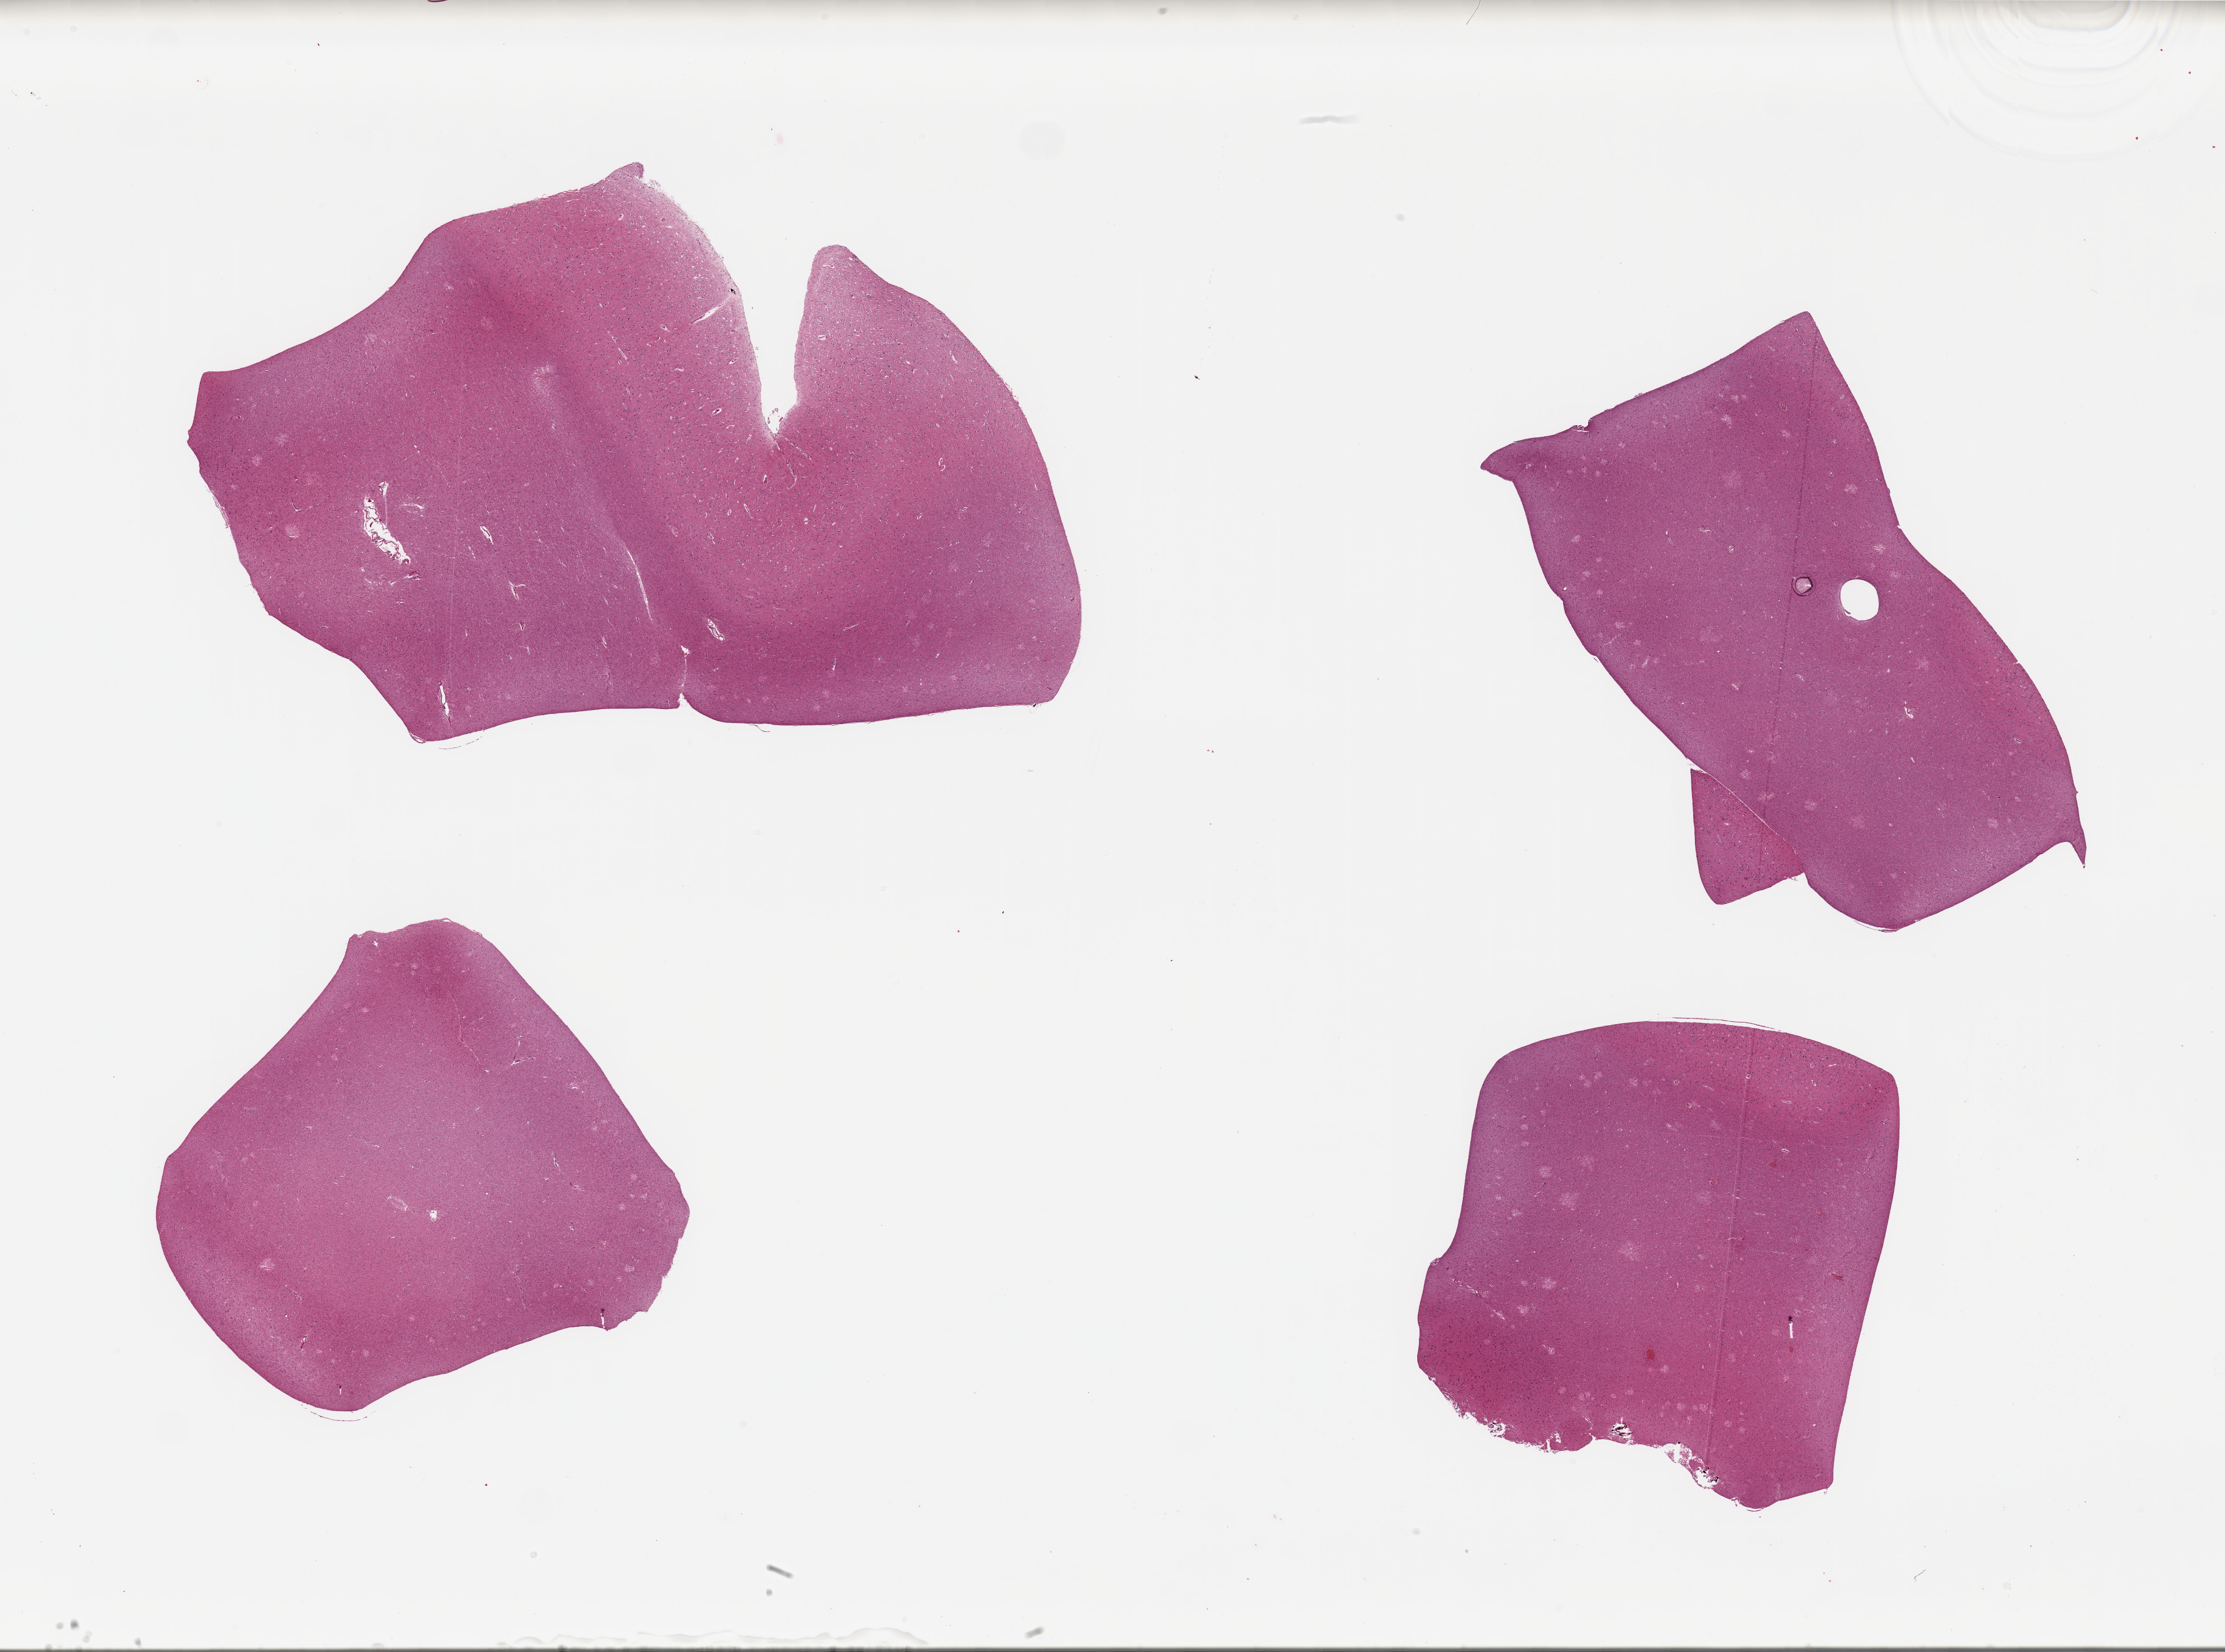
H&E whole-slide image — shown as a low-resolution overview of the whole scanned area (about 31.5 x 23.4 mm); PAXgene-fixed paraffin-embedded (PFPE) section; target tissue: cerebral cortex; donor tissue sample. Male donor.
• reviewer comment on this tissue sample: 4 pieces